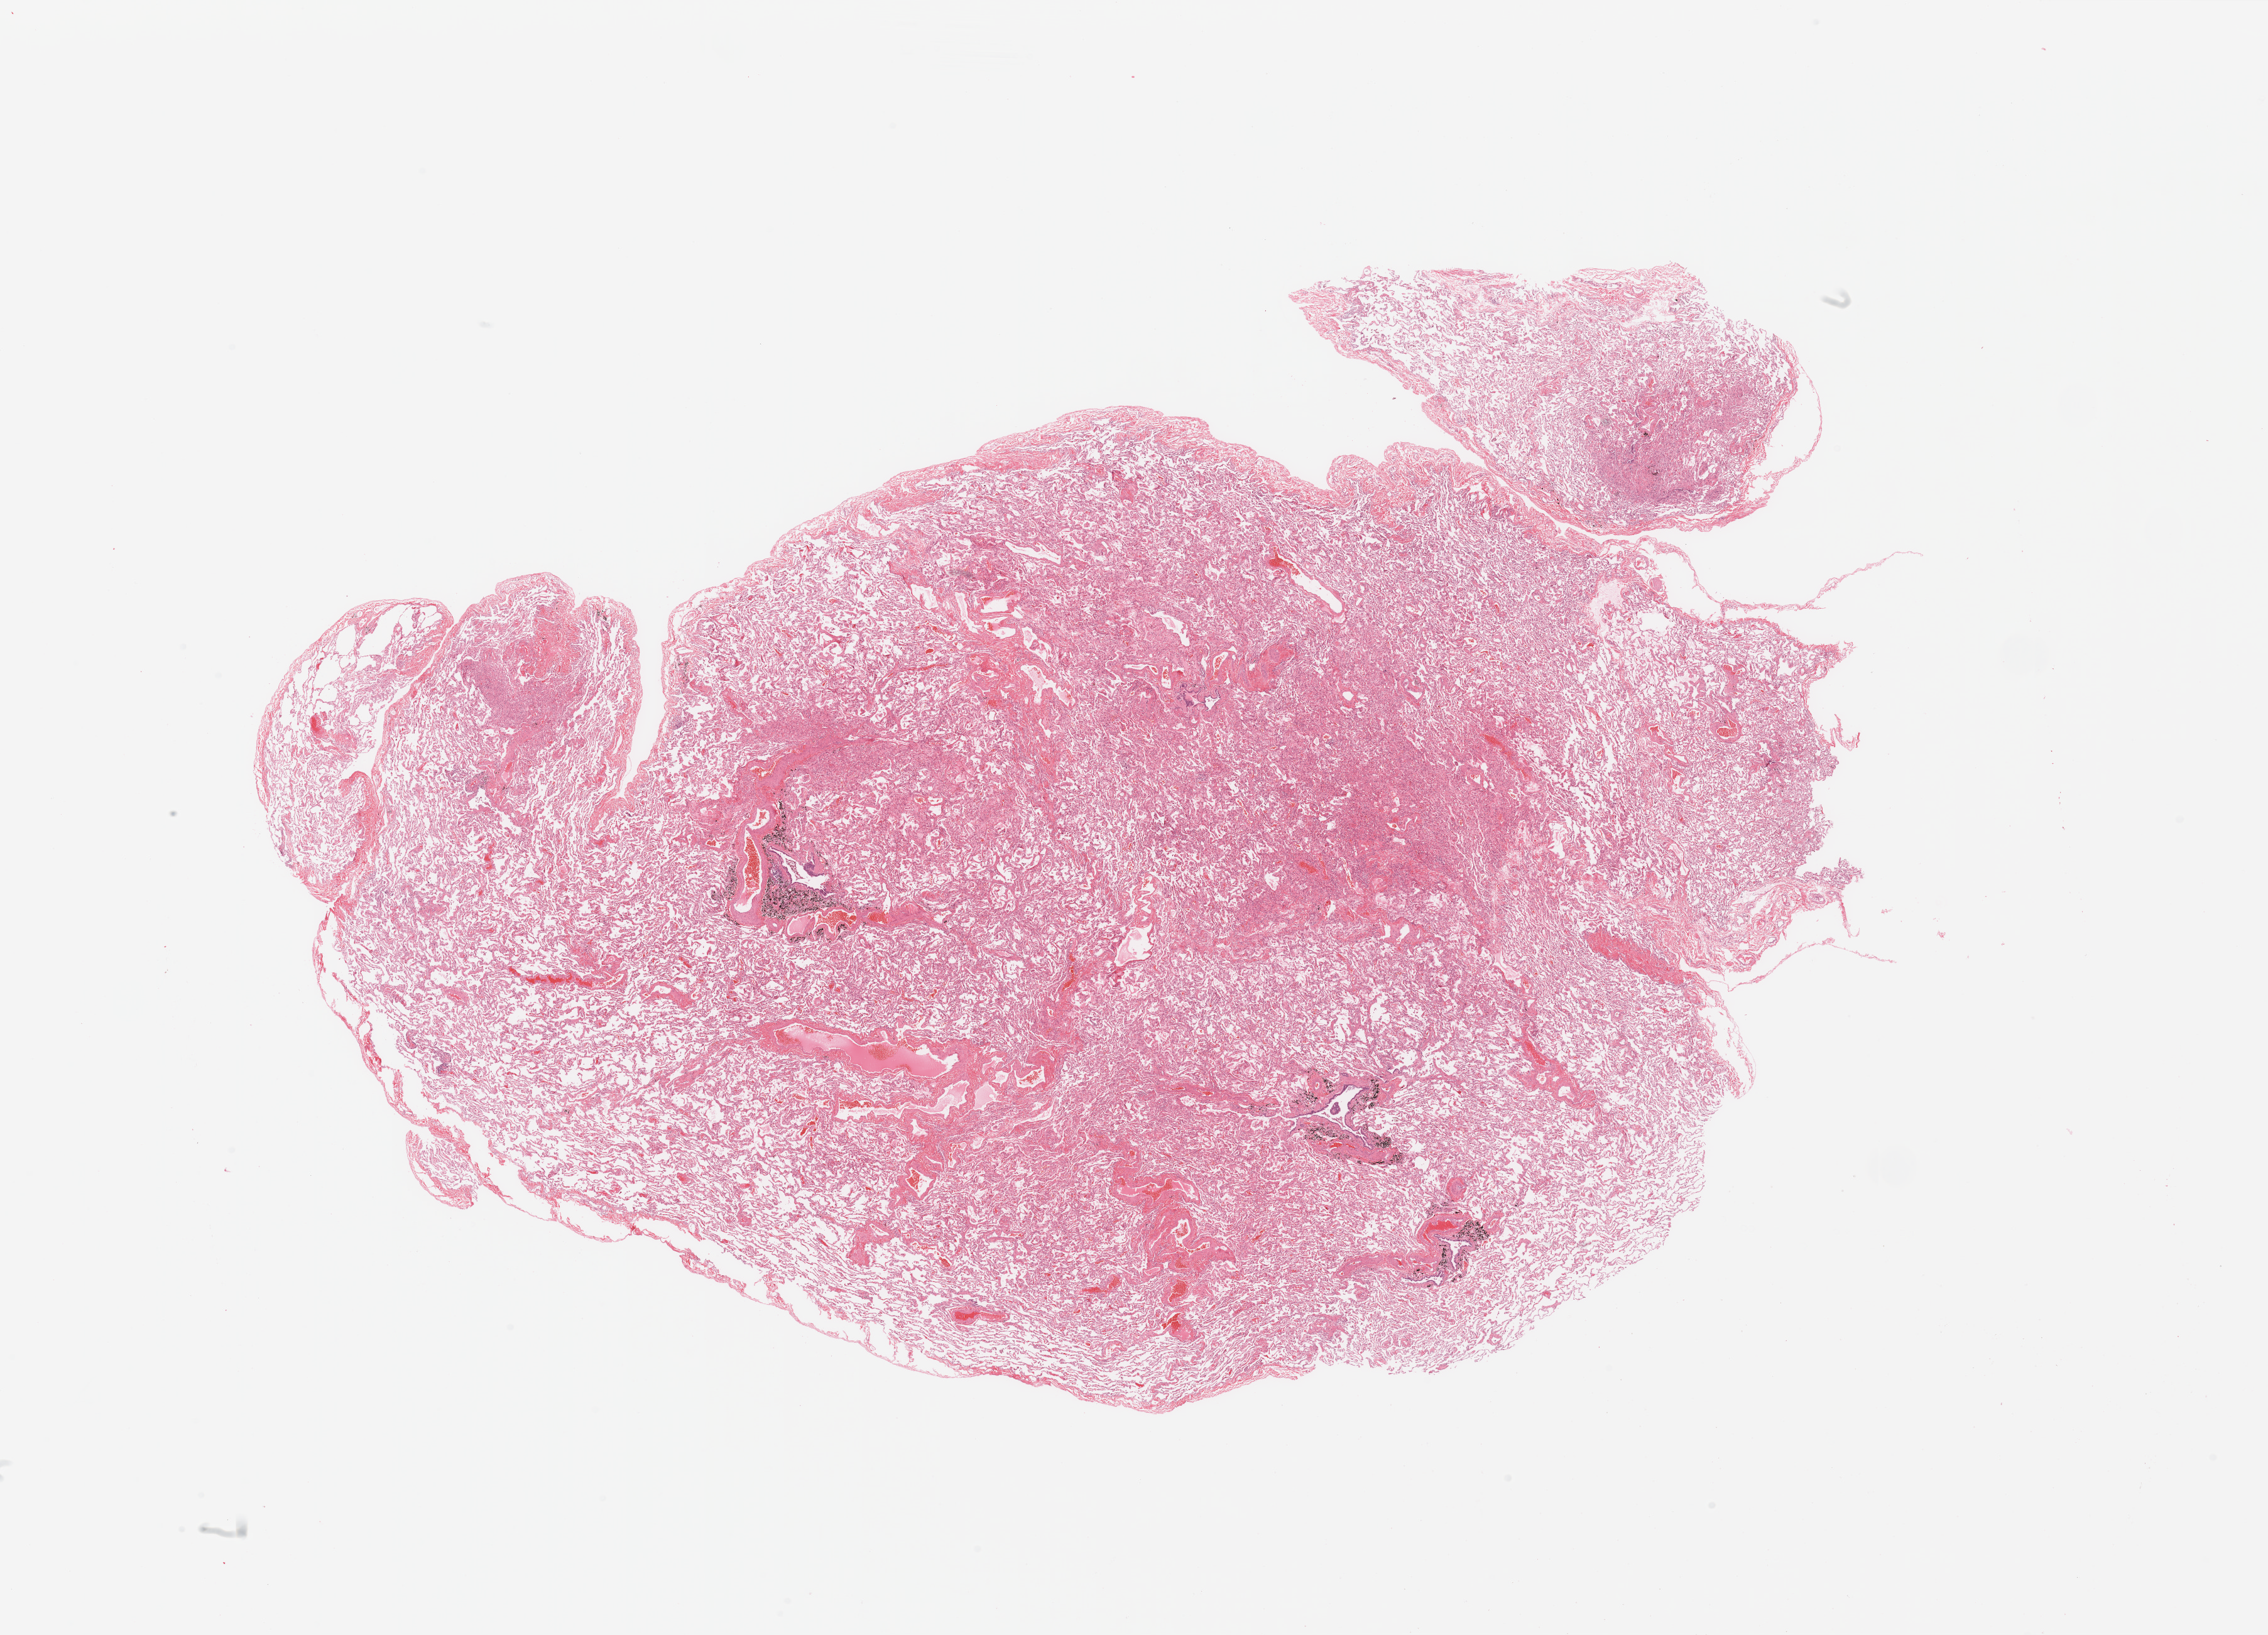
Hematoxylin and eosin (H&E) stained whole-slide image — low-resolution overview of the scanned area, about 28.5 x 20.6 mm, normal (non-tumour) tissue sample, sampled site: lung. Patient: female, age 48 years.
This section: normal (non-tumour) tissue from the same patient. Patient diagnosis: Adenocarcinoma, NOS.